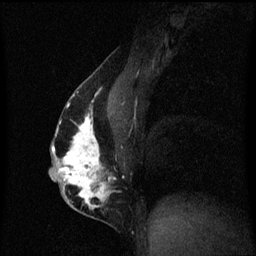
Breast MRI (dynamic contrast-enhanced), one sagittal slice. Slice 32 of 60 in the series (ordered by position). Dynamic contrast-enhanced series, image 2 of 3 at this slice position (ordered by acquisition). 1.5 T. TE 4.2 ms, TR 8.4 ms. 256 × 256 image matrix, field of view 200 × 200 mm. Patient: female, 40 years.
Outlined on this slice (semi-automatic segmentation, software-assisted and operator-edited):
- analysis volume of interest (the breast-tissue region the enhancement analysis was run in; not a lesion): bounding box (x1, y1, x2, y2) in pixels: (50, 84, 118, 211)
- tumour enhancement mask (voxels above the 70 % enhancement threshold inside the analysis volume of interest): (50, 88, 113, 211)